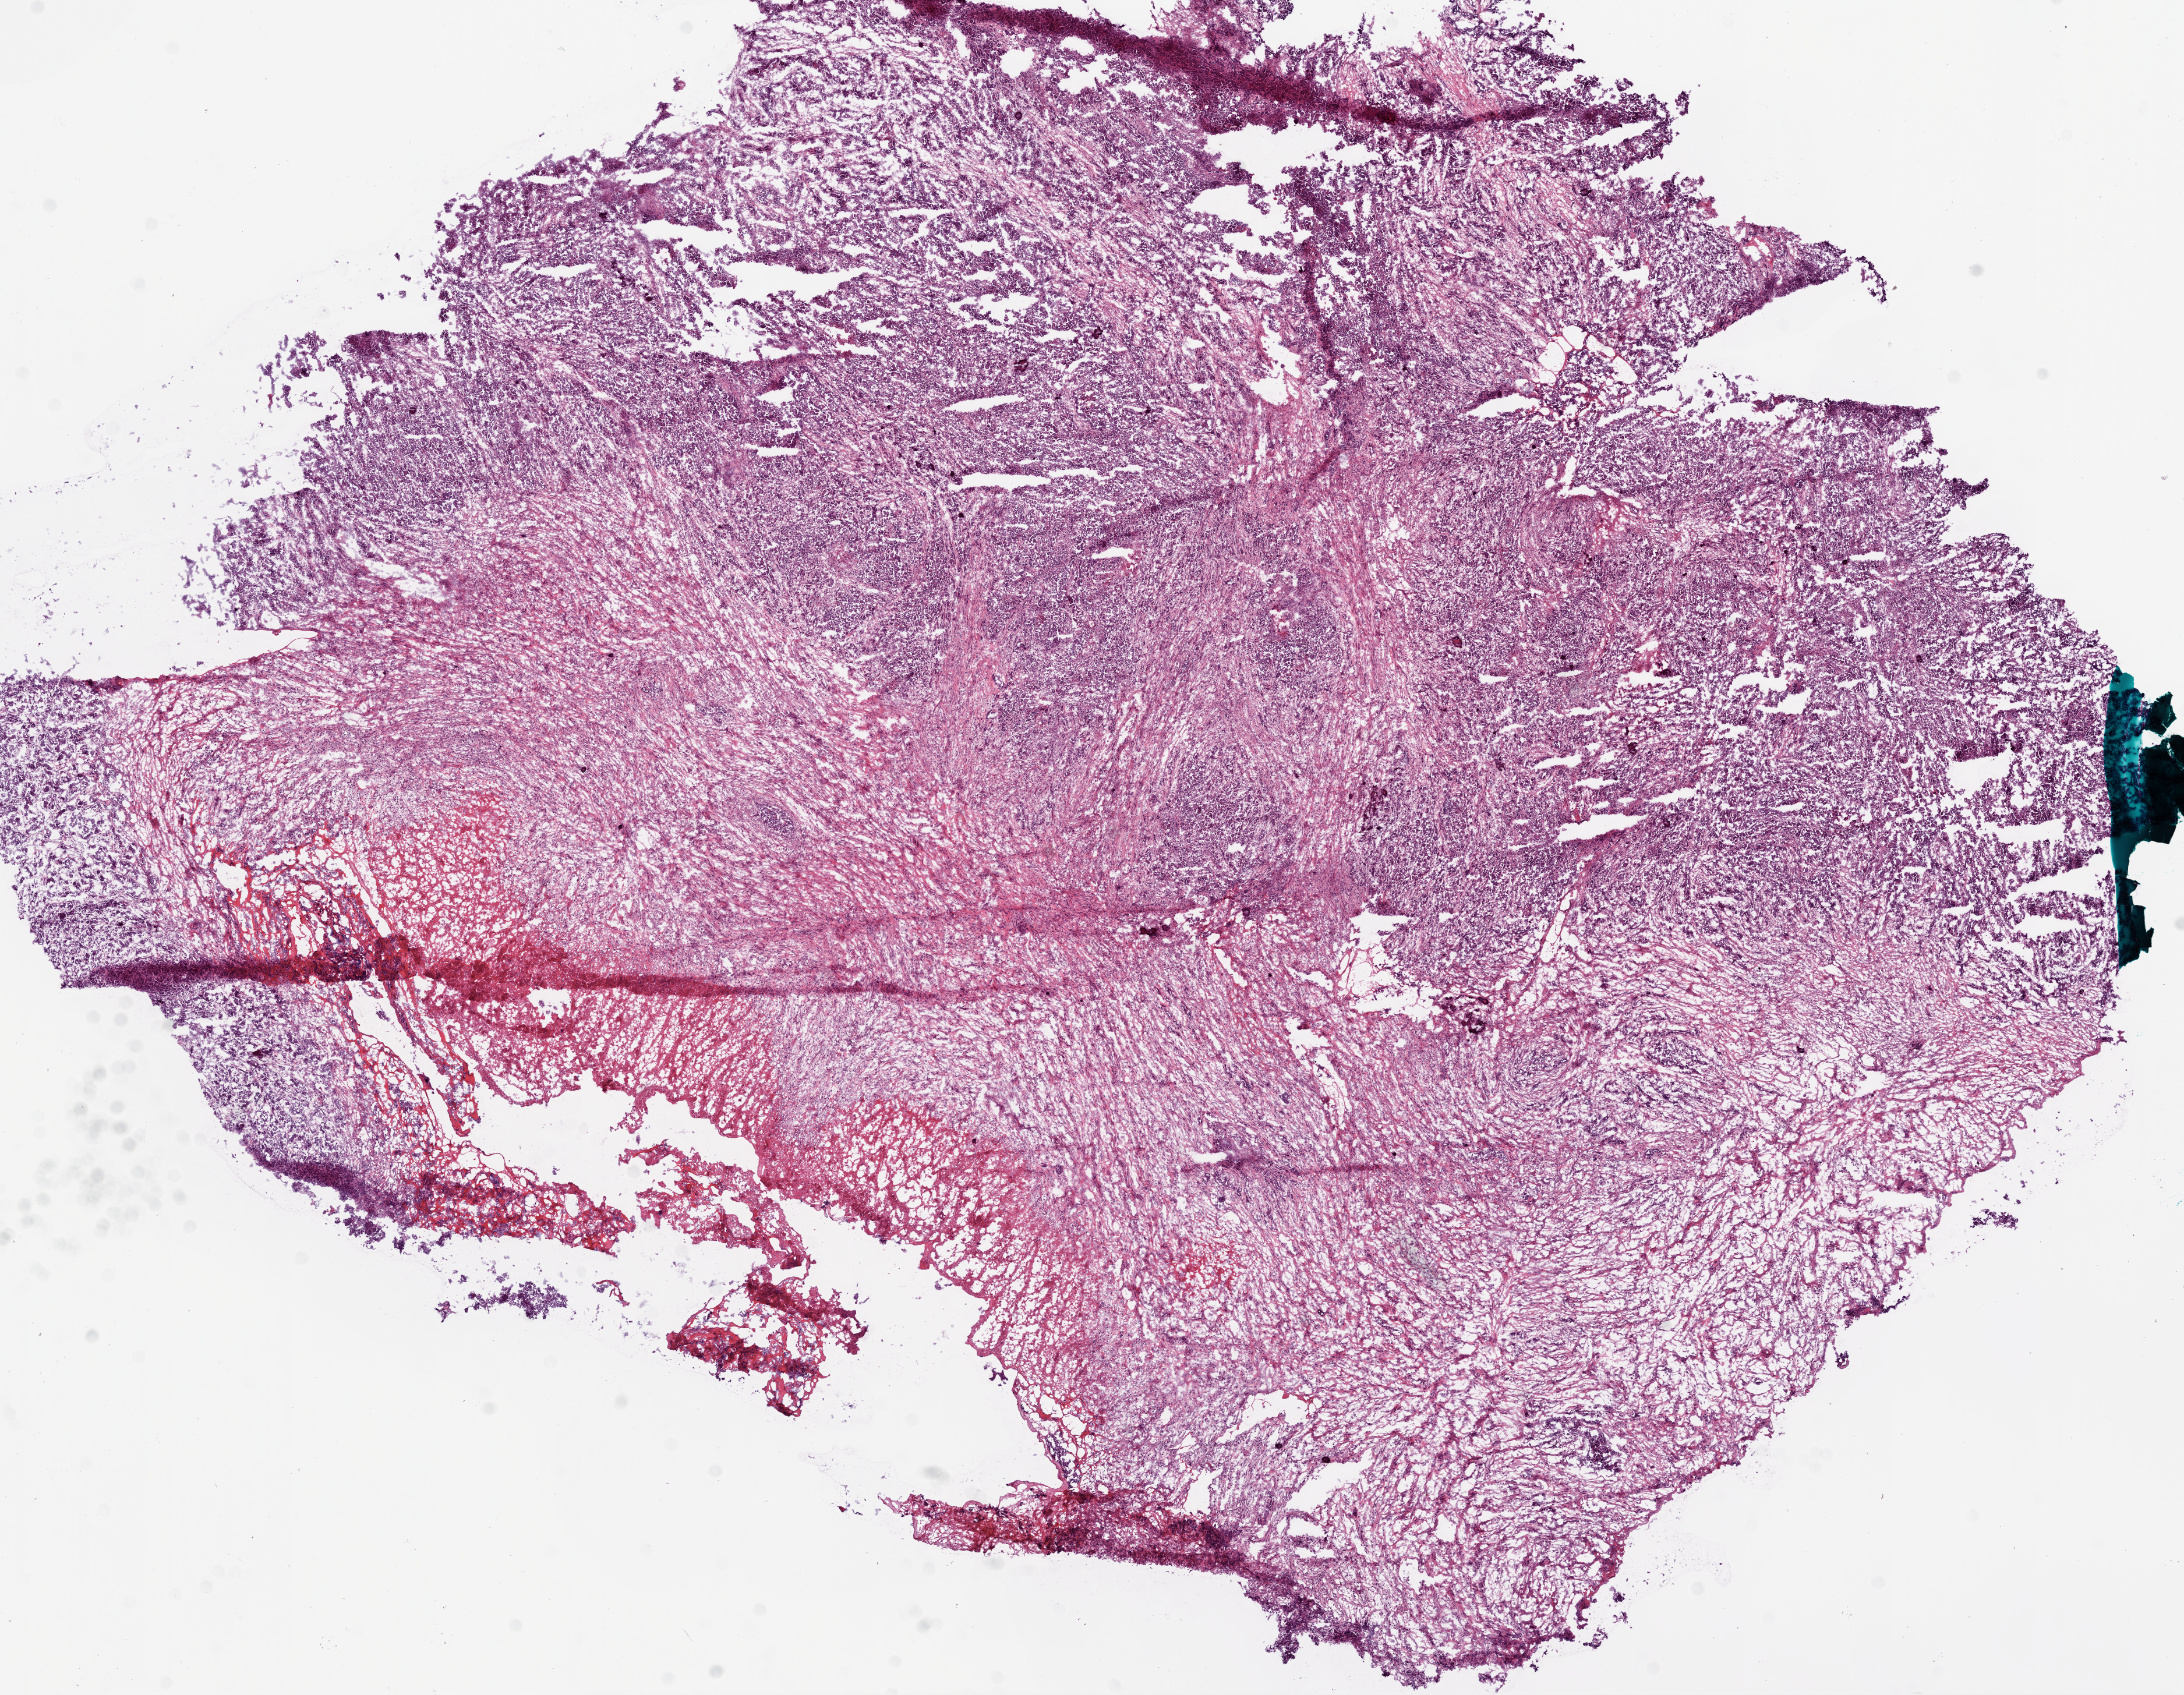
Digitized H&E tissue section (whole slide), shown as a low-resolution overview of the whole scanned area (about 15.0 x 11.7 mm). Frozen section from the bottom of the tissue portion. Sample: primary tumour, ovary. Female patient; age at initial diagnosis 59 years. Histologic grade: G3 (poorly differentiated). Pathologist review of this section (percent, as recorded): tumour cells 75%, tumour nuclei 80%, normal cells 0%, stromal cells 20%, necrosis 5%.
Histologic diagnosis: Serous cystadenocarcinoma, NOS. FIGO stage: IIIC. Laterality: bilateral.